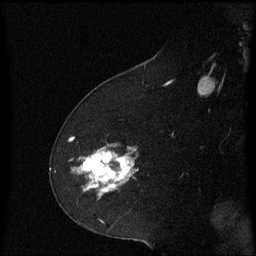
Breast MRI (dynamic contrast-enhanced), one sagittal slice. Slice 37 of 60 in the series (ordered by position). Dynamic contrast-enhanced series, image 2 of 3 at this slice position (ordered by acquisition). 1.5 T. TE 4.2 ms, TR 8.4 ms. 2.2 mm slice thickness. 256 × 256 image matrix, field of view 200 × 200 mm. Patient: female, 60 years. Case-level facts recorded for this patient, not image findings: setting: breast cancer imaged before/during neoadjuvant chemotherapy; receptor status: triple-negative.
Structures marked on this image (semi-automatic segmentation, software-assisted and operator-edited):
- analysis volume of interest (the breast-tissue region the enhancement analysis was run in; not a lesion): bounding box <72,142,139,201> (left, top, right, bottom; pixels)
- tumour enhancement mask (voxels above the 70 % enhancement threshold inside the analysis volume of interest): <77,148,135,191>